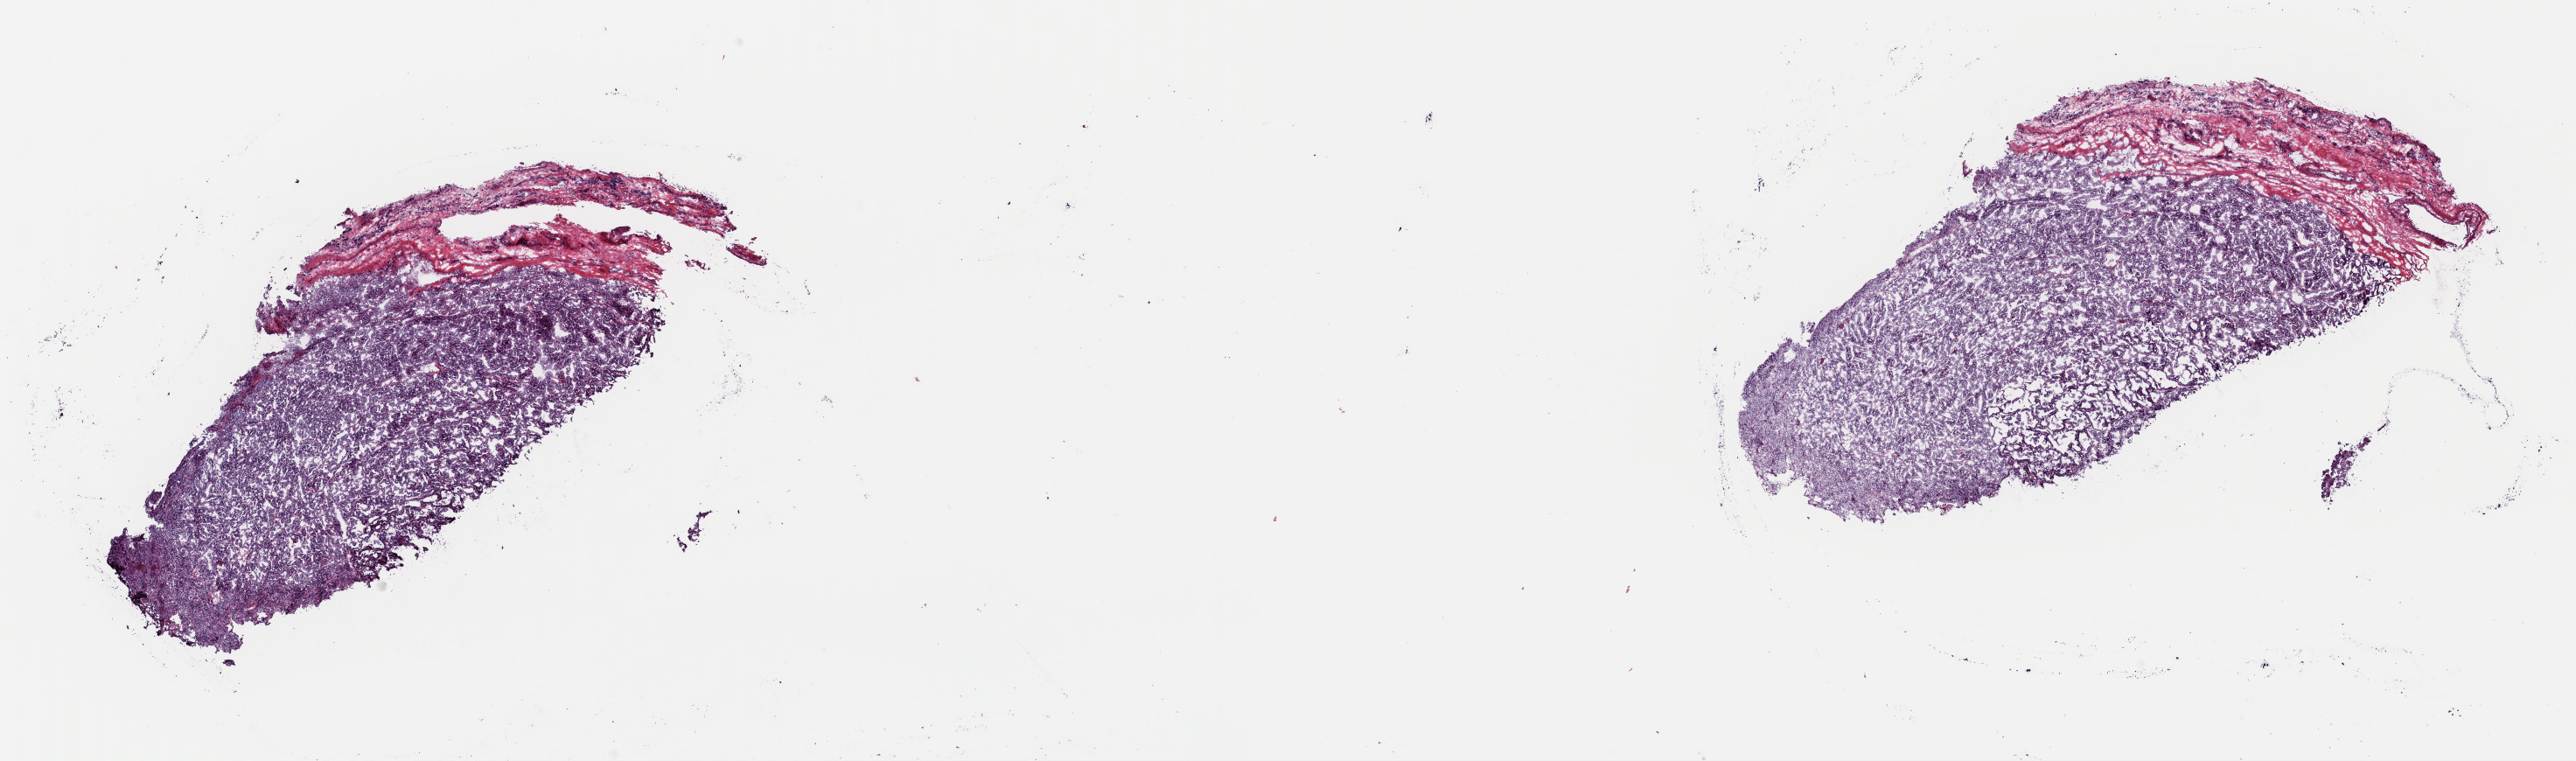
Digitized Hematoxylin and eosin (H&E) stained tissue section (whole slide) — low-resolution overview of the scanned area, about 23.3 x 6.9 mm (slide scanned at 40x). Frozen section from the top of the tissue portion. Thyroid, primary tumour sample. Patient: male, age at initial diagnosis 15 years. Slide review estimates, as recorded: tumour cells 90%, tumour nuclei 100%, normal cells 0%, stromal cells 10%, necrosis 0%. Infiltration values recorded for this section: lymphocyte infiltration 1%, monocyte infiltration 1%, neutrophil infiltration 0%.
Pathologic diagnosis: Papillary adenocarcinoma, NOS (thyroid gland). Laterality: left. TNM: T3 N0 M0. AJCC pathologic stage: I (6th edition).